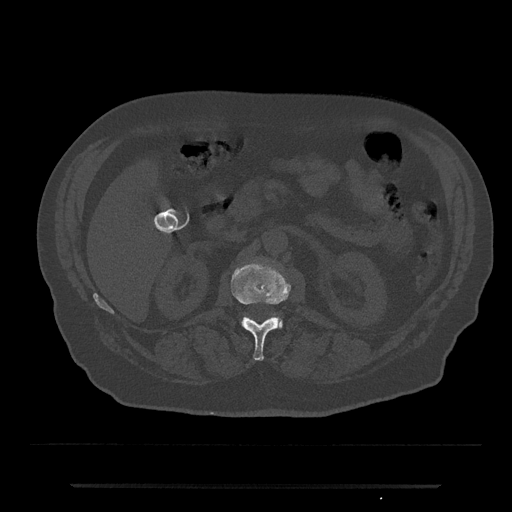
CT including the spine, one axial slice; slice 520 of 797 in the series (ordered by position); reconstruction kernel Br40s/3; bone window (W 1800 / L 400 HU); 512 × 512 image matrix, field of view 434 × 434 mm. Male patient, age 80 years. From the clinical record (not read from this slice): primary cancer: prostate.
Structures marked on this image (semi-automatically segmented with operator editing):
- L1 vertebra: box from (x=231, y=262) to (x=290, y=361) px
- L2 vertebra: (x=274, y=315)–(x=283, y=329)